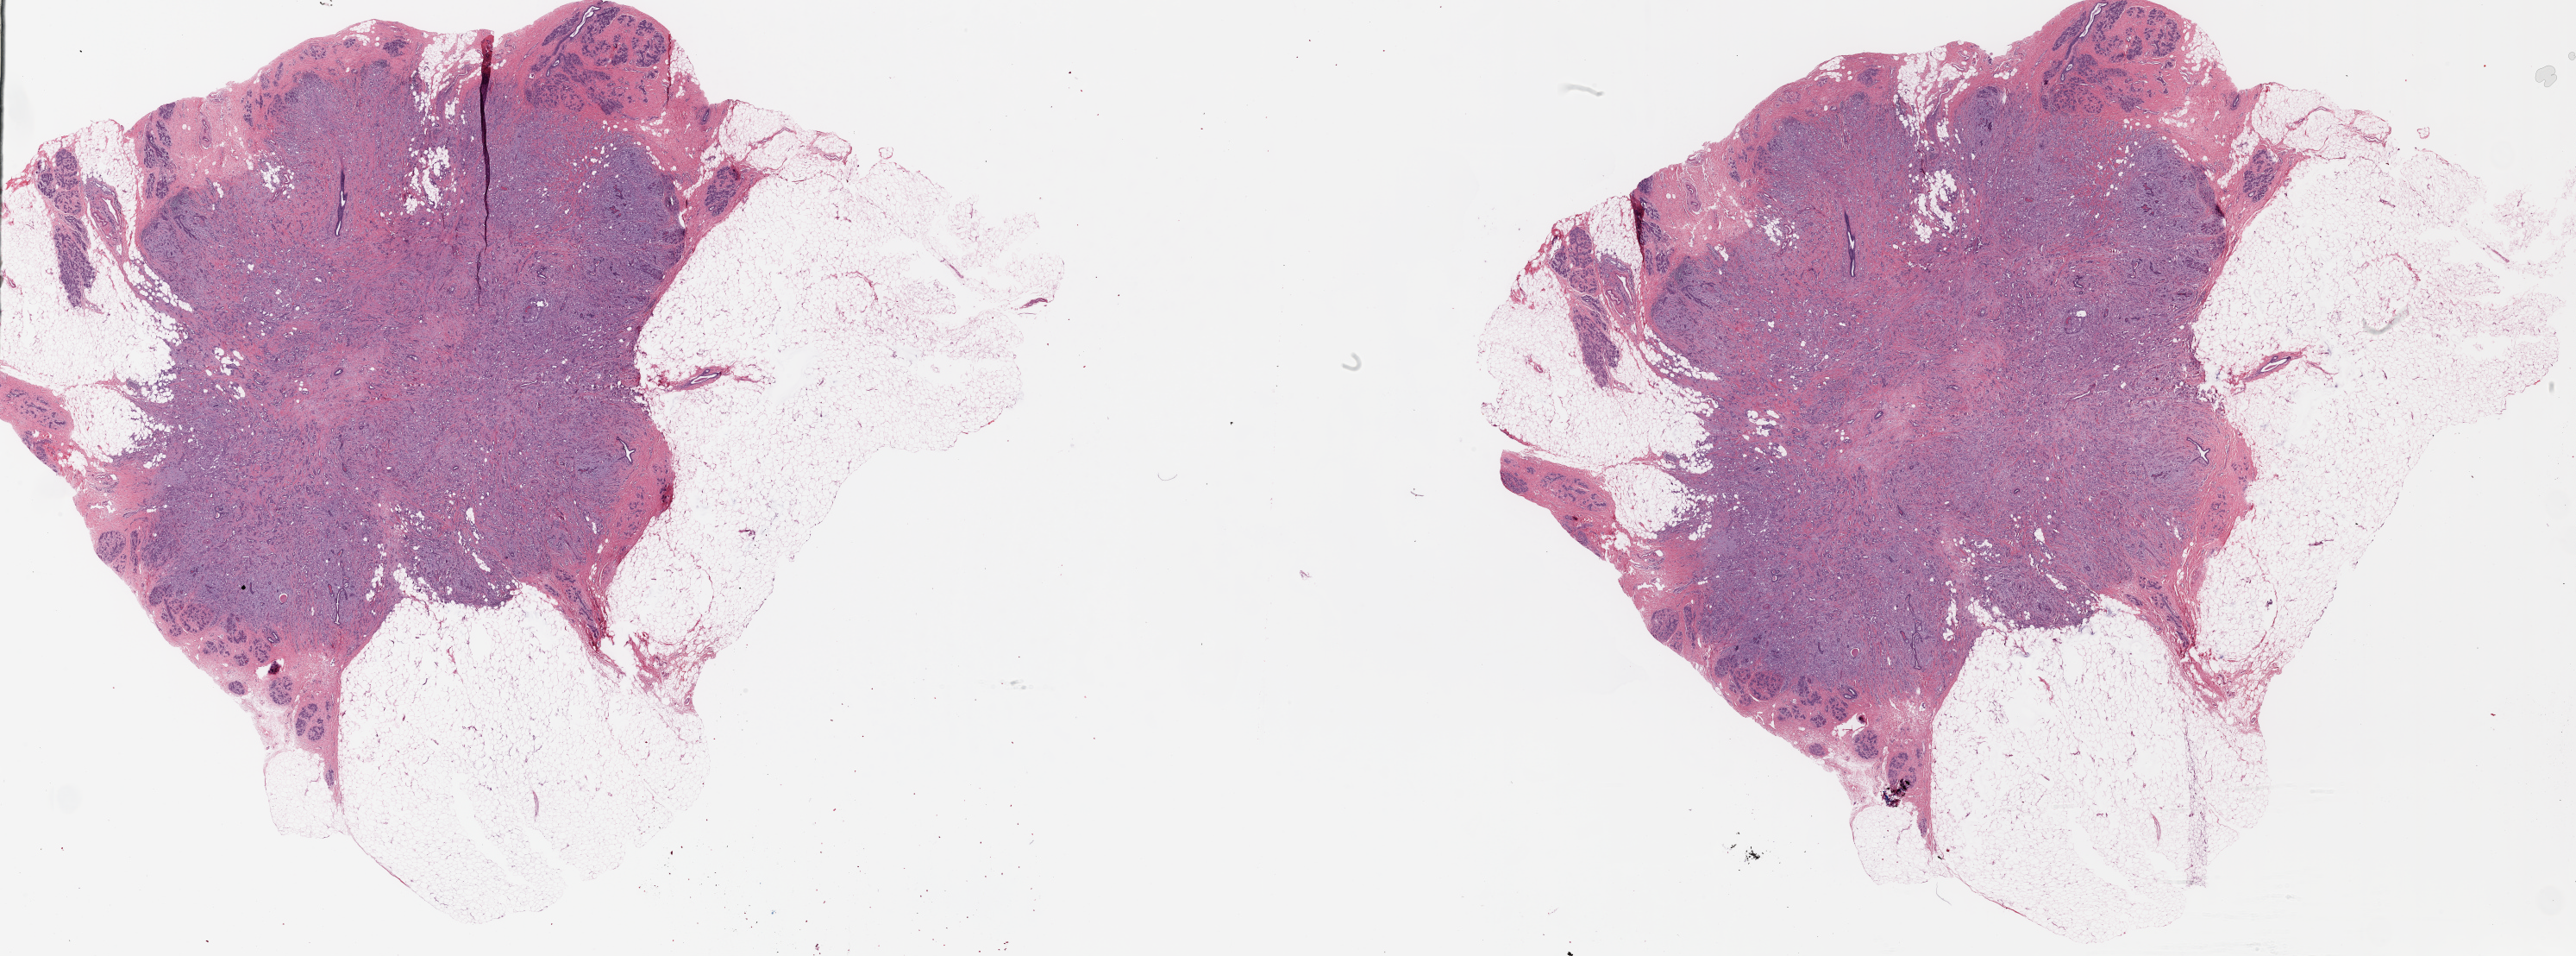
H&E-stained whole-slide image — whole scanned area (about 47.7 x 17.7 mm, from a 20x scan) shown as a low-resolution overview; formalin-fixed paraffin-embedded (FFPE) diagnostic section; sample: primary tumour, breast. Female patient; age at initial diagnosis 42 years.
Pathologic diagnosis: Infiltrating duct carcinoma, NOS.